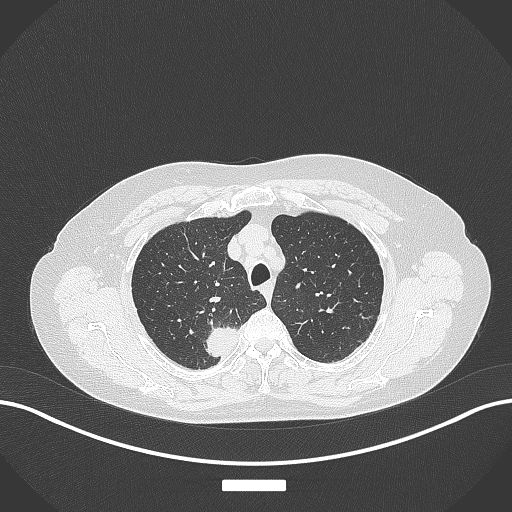
Chest CT, one axial slice. Position 313 of 357 along the scan axis. Reconstruction kernel B70f. Lung window (W 1500 / L -600 HU). 1 mm slice thickness. 512 × 512 image matrix, field of view 400 × 400 mm. Patient: female, 62 years. From the clinical record (not read from this slice): clinical TNM (as recorded): T1c N1 M0.
Outlined on this slice (bounding box drawn by a radiologist):
- lung tumour (recorded histology: squamous cell carcinoma): bounding box (x1, y1, x2, y2) in pixels: (201, 320, 238, 360)